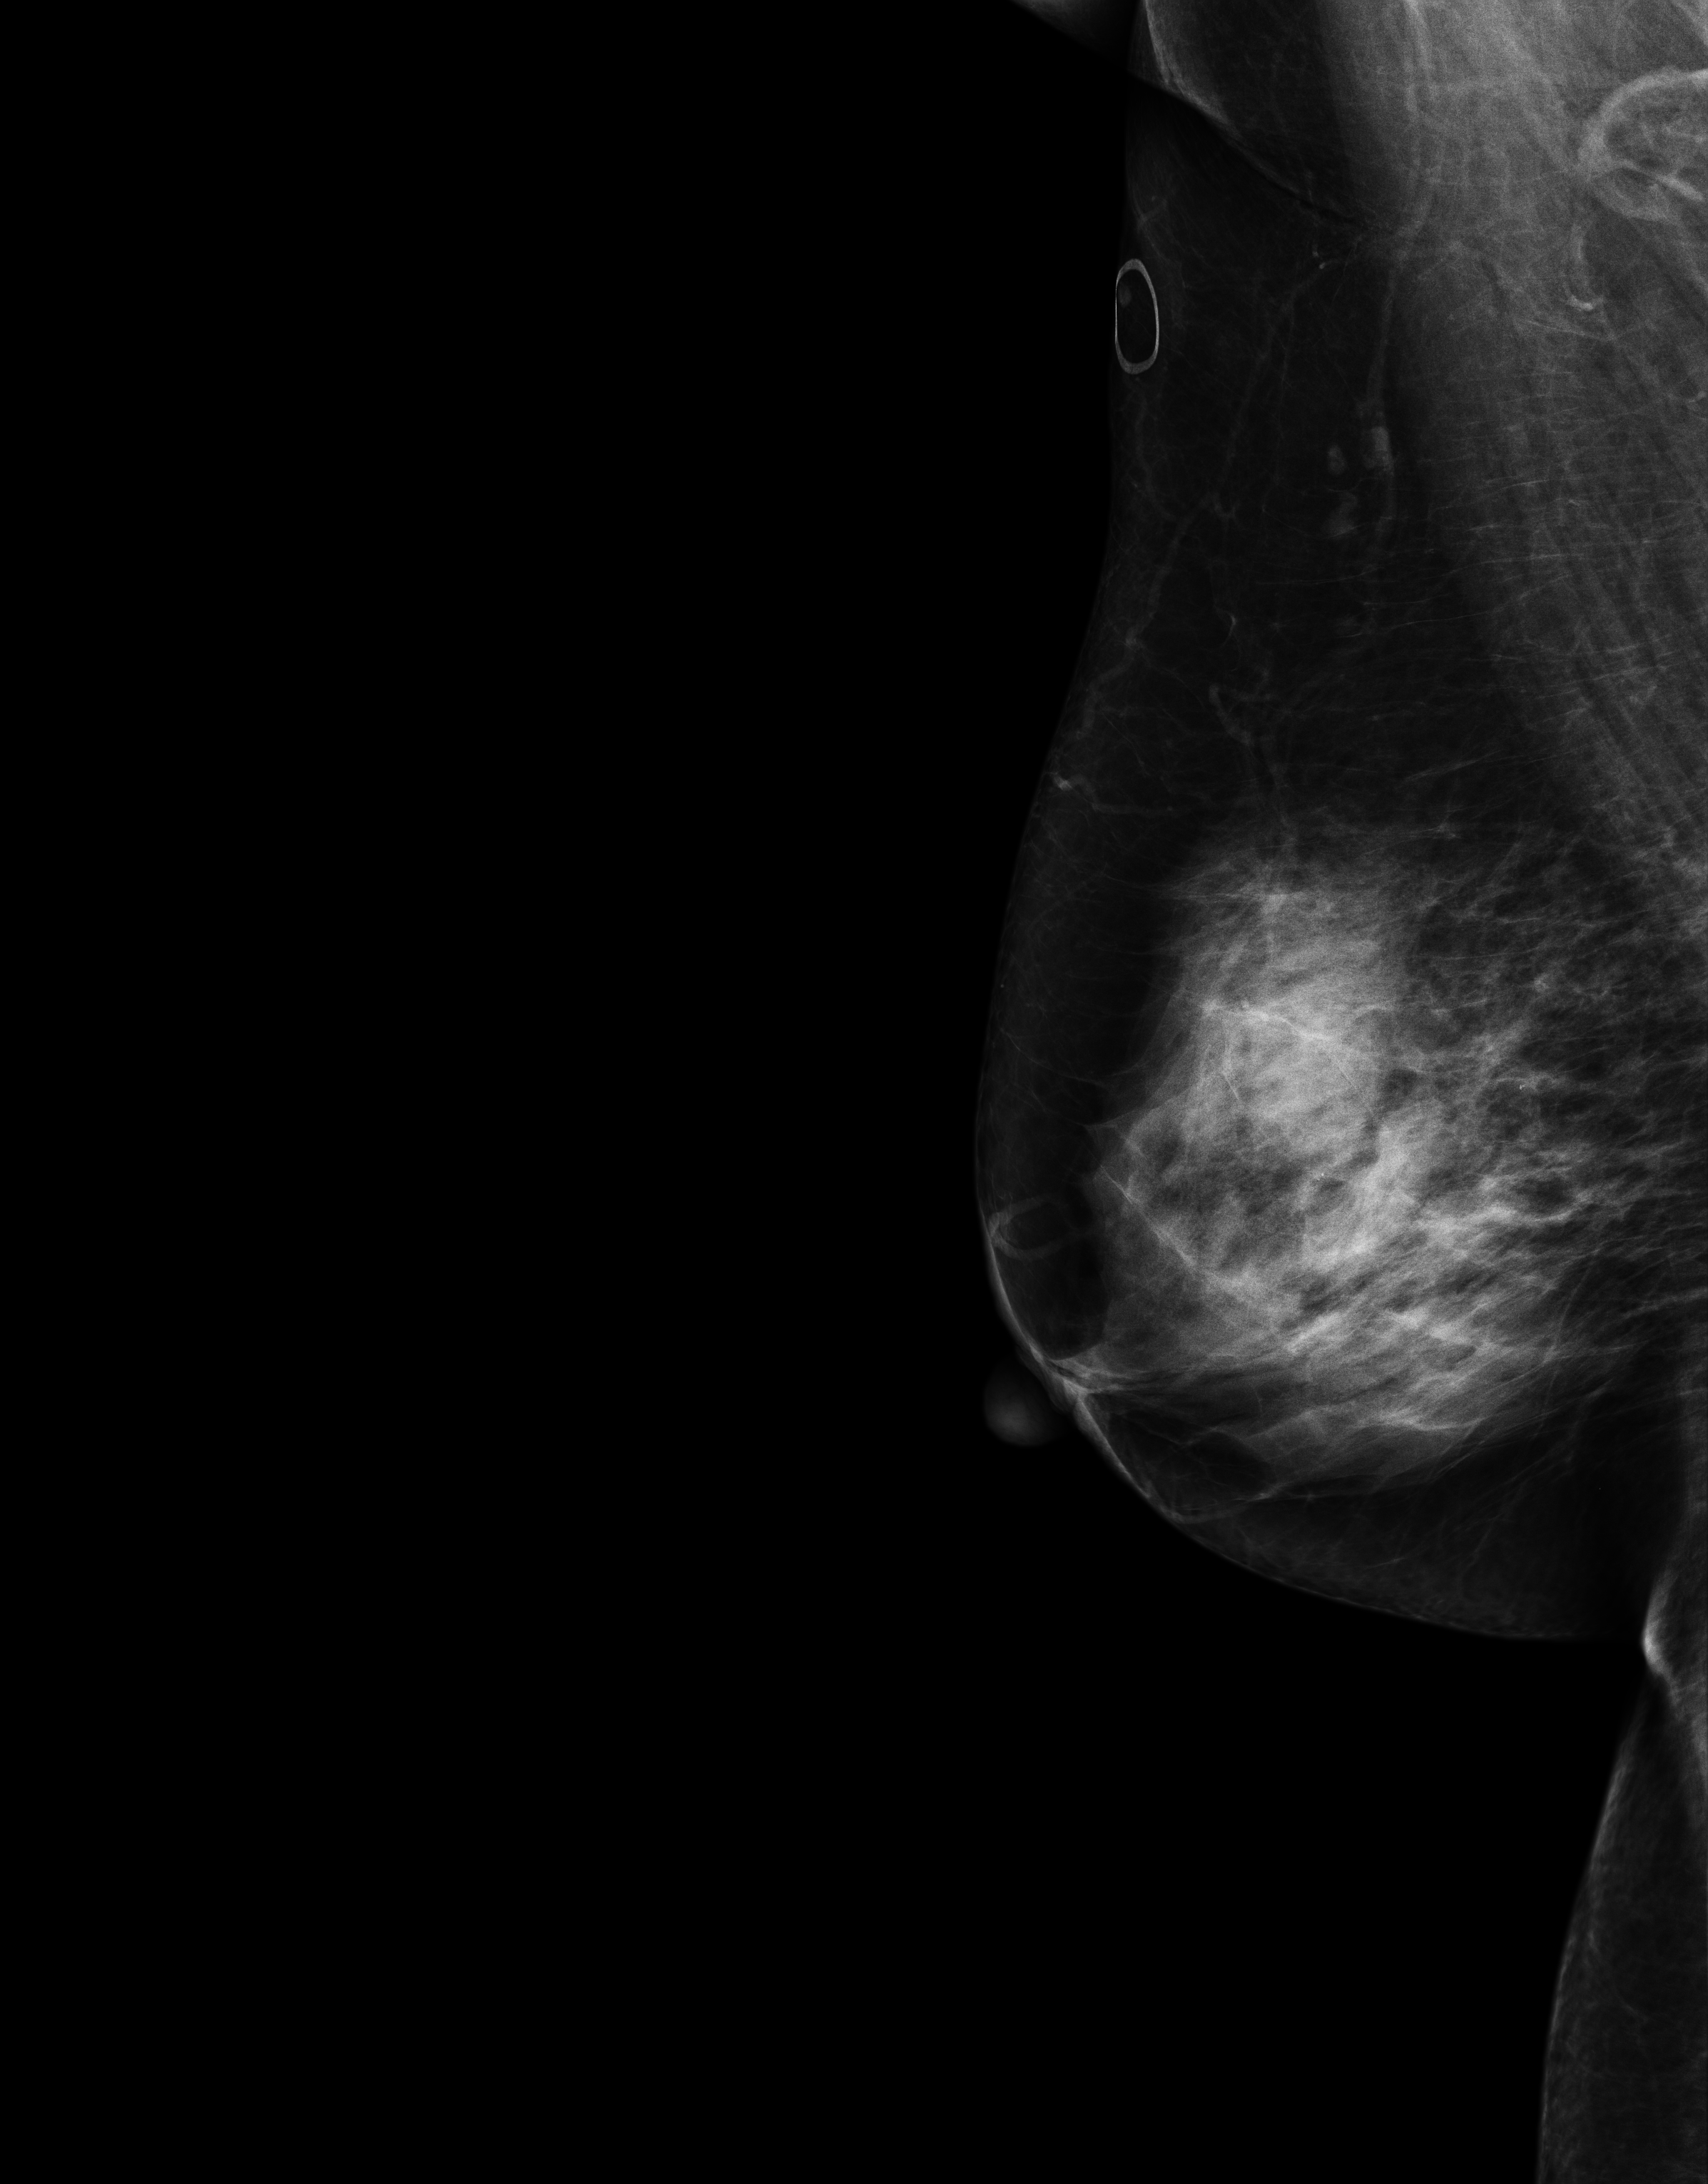
Digital mammogram (FFDM); right breast; MLO view; annual screening mammography examination; compressed breast thickness 65 mm. Patient: female, 67 years.
BI-RADS breast density category at the screening exam (both breasts, scale 1–4): 3. Final BI-RADS category for the screening round (tomosynthesis exam, both breasts): category 1. Recall: no recall after this screen.